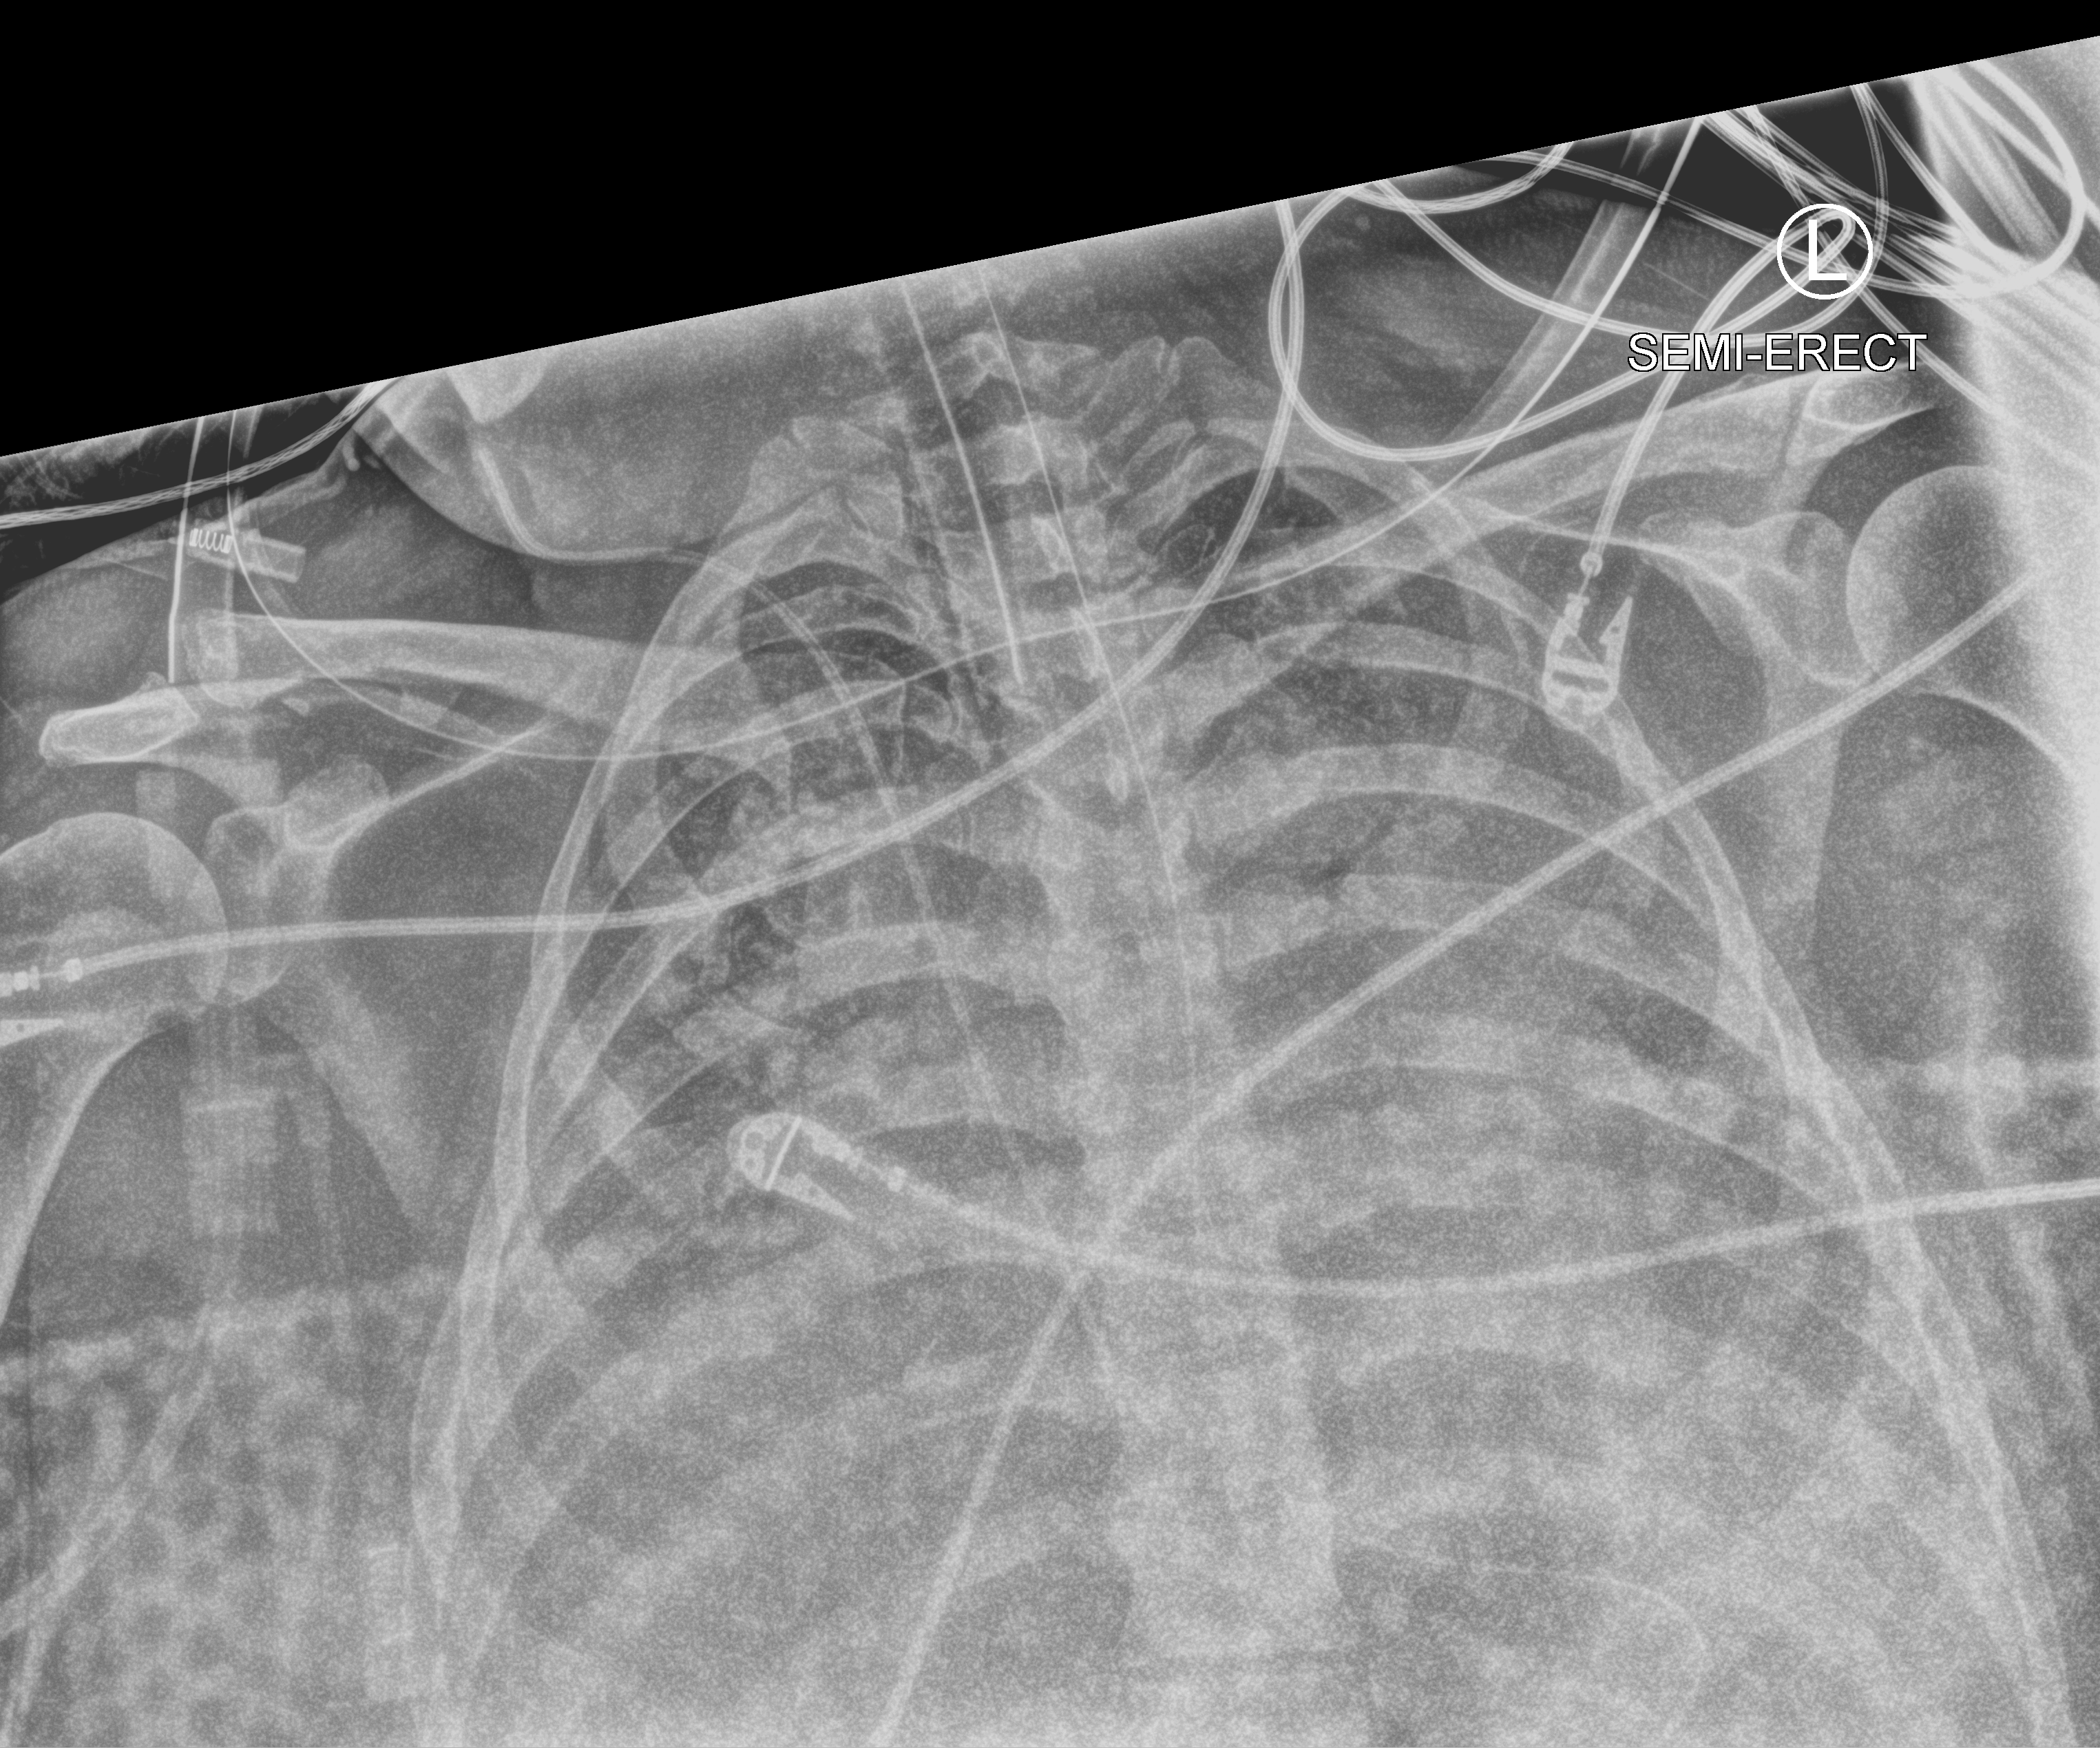
Portable chest radiograph, anteroposterior (AP) projection. Patient hospitalised with COVID-19; female, aged 18–59 years.
From the hospital-stay record, not from the radiograph (when in the stay this image was taken is not recorded): length of hospital stay: 25 days; admitted to intensive care during this hospital stay: yes.